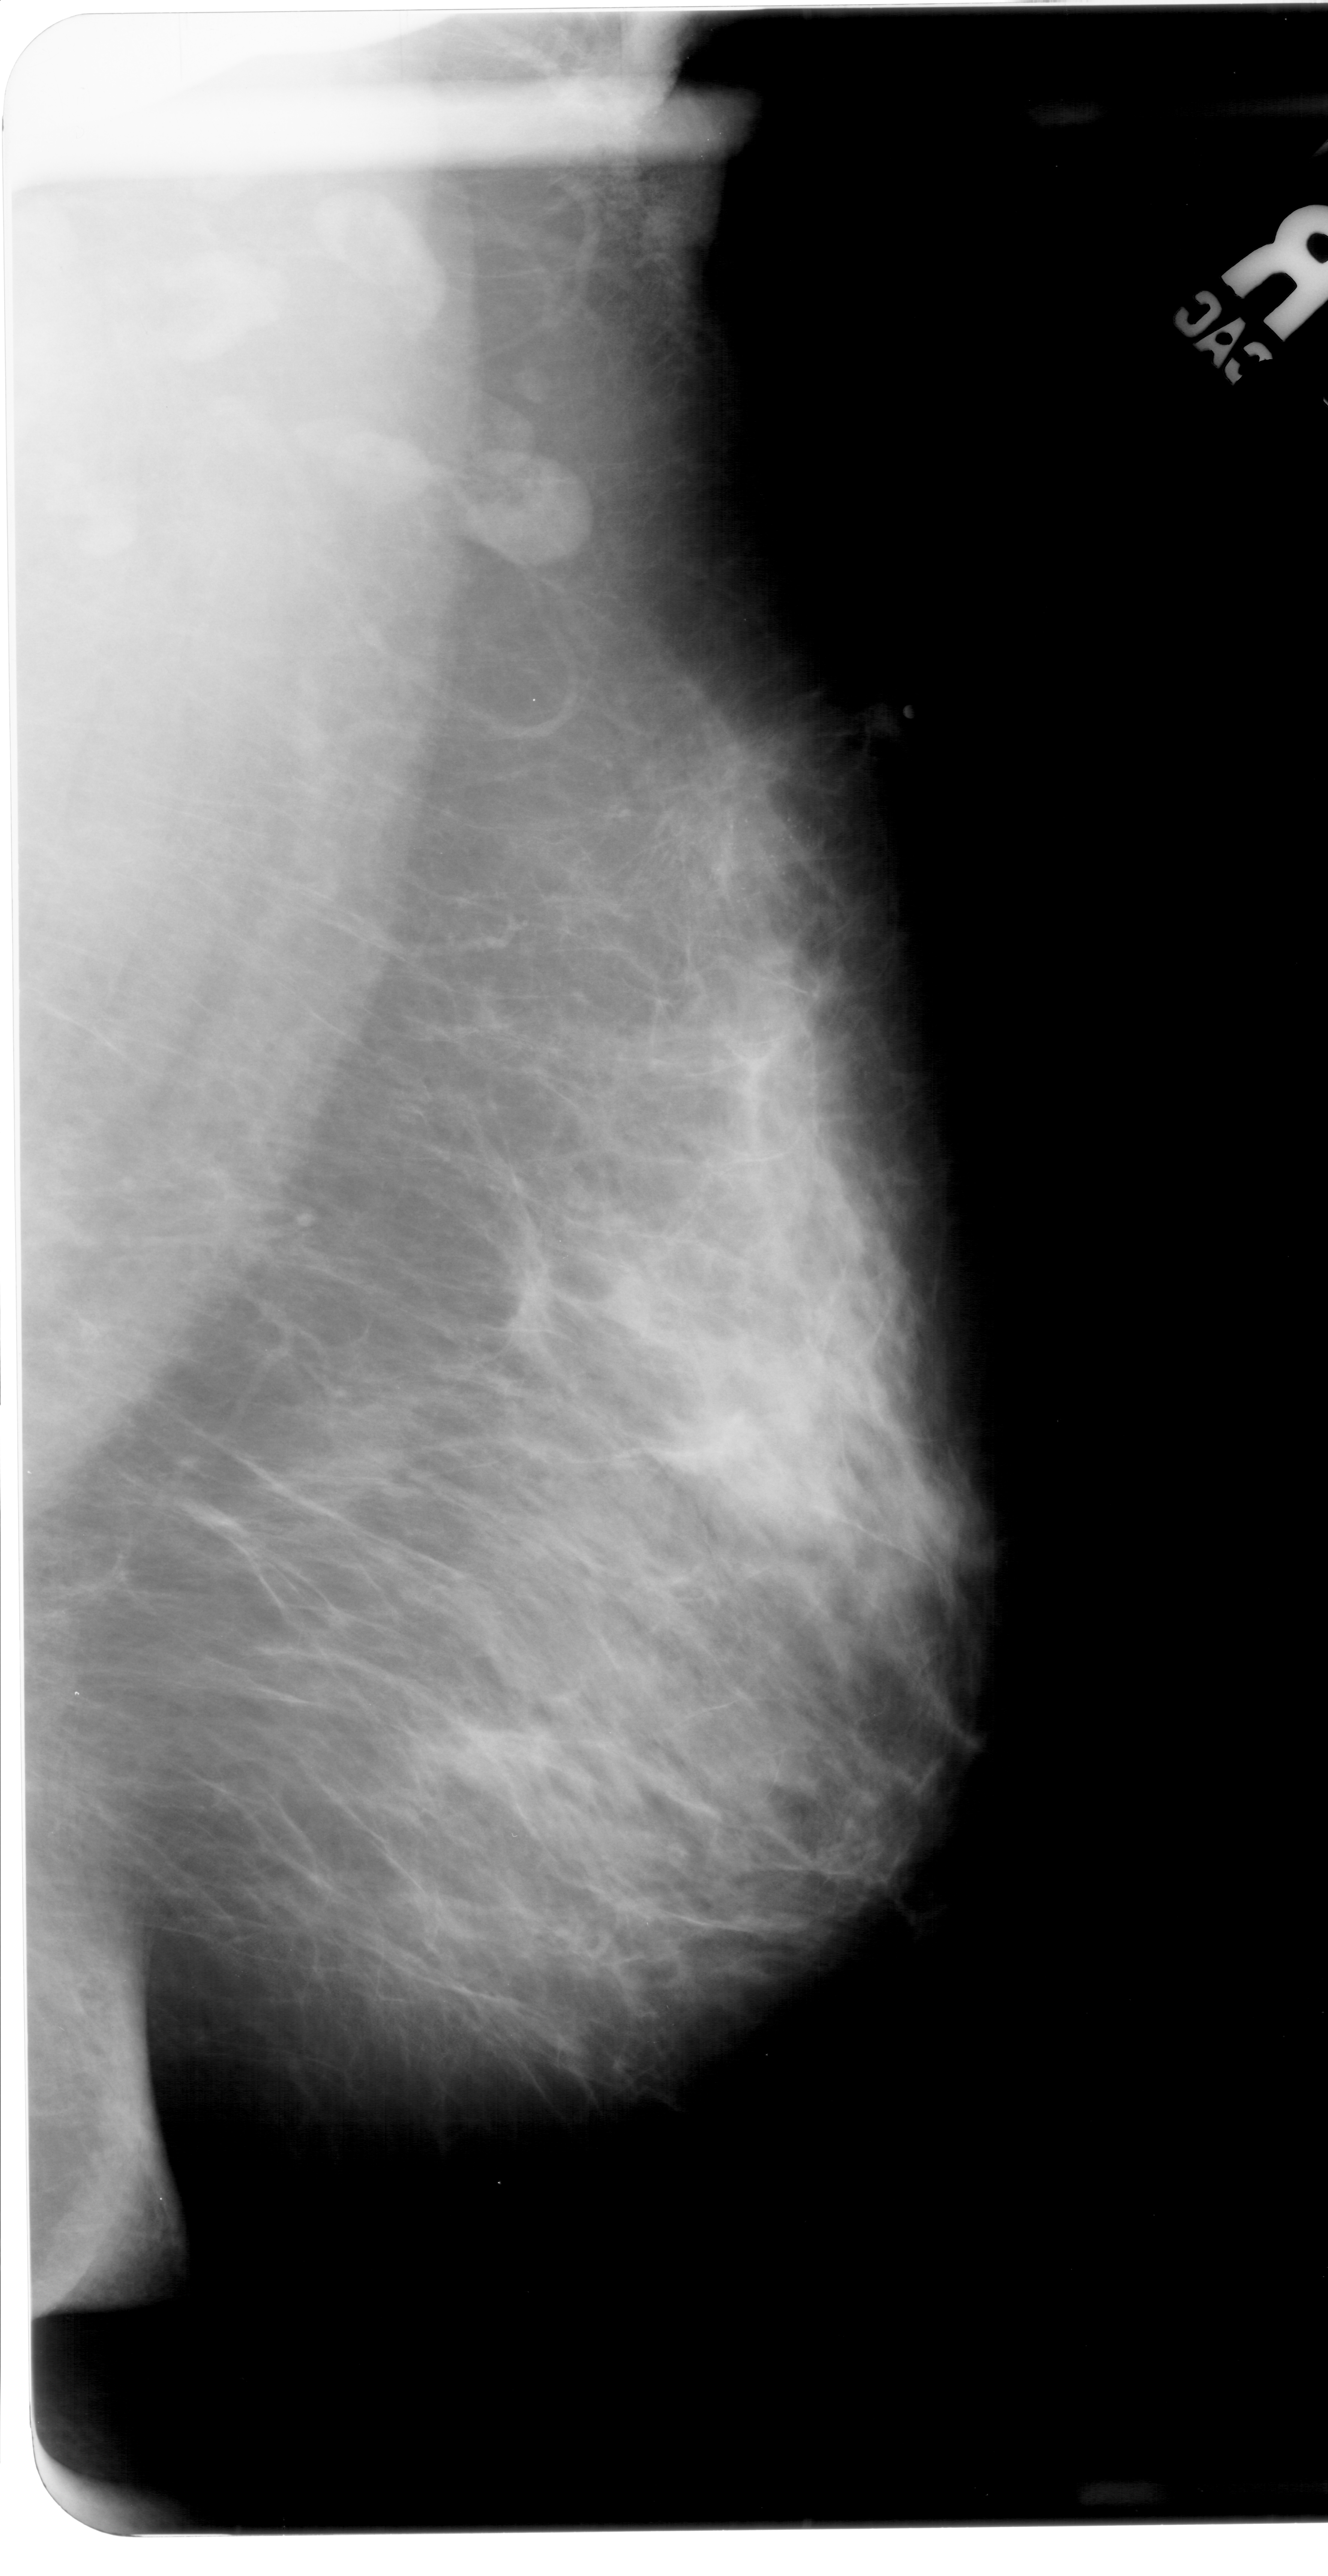
Mammogram (digitized film), right breast, MLO view, BI-RADS breast density category 3 (scale 1–4).
Abnormality record for this image: mass, shape irregular, margins spiculated; BI-RADS assessment category 5; subtlety rating 4 on a 1 (subtle) to 5 (obvious) scale; pathology (as recorded): malignant.